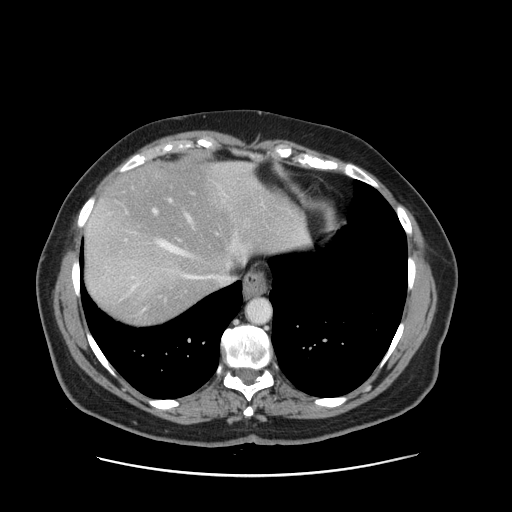
Contrast-enhanced abdominal CT, one axial slice. Position 129 of 161 along the scan axis. 120 kVp. Intravenous contrast given. Soft-tissue window (W 400 / L 40 HU). 512 × 512 image matrix, field of view 398 × 398 mm. Female patient, age 62 years. Case-level facts recorded for this patient, not image findings: diagnosis: colorectal cancer liver metastases, imaged before liver resection.
Outlined on this slice (expert manual segmentation):
- hepatic veins: bounding box [x1, y1, x2, y2] px = [127, 165, 250, 290]
- liver: [84, 162, 305, 325]
- planned liver remnant (the part of the liver to remain after resection): [94, 162, 304, 279]
- portal vein (with intrahepatic branches): [153, 193, 193, 241]